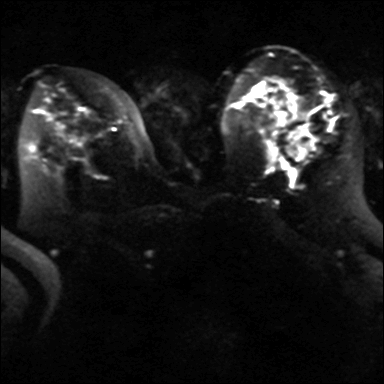
Breast MRI, one axial slice. Position 22 of 40 along the scan axis. Diffusion-weighted series; image 2 of 4 stored at this slice position (different b-values; order by instance number). 3 T. 384 × 384 image matrix, field of view 320 × 320 mm. Female patient.
Outlined on this slice (expert manual segmentation):
- tumour on diffusion-weighted imaging: bounding box [x1, y1, x2, y2] px = [287, 125, 314, 161]